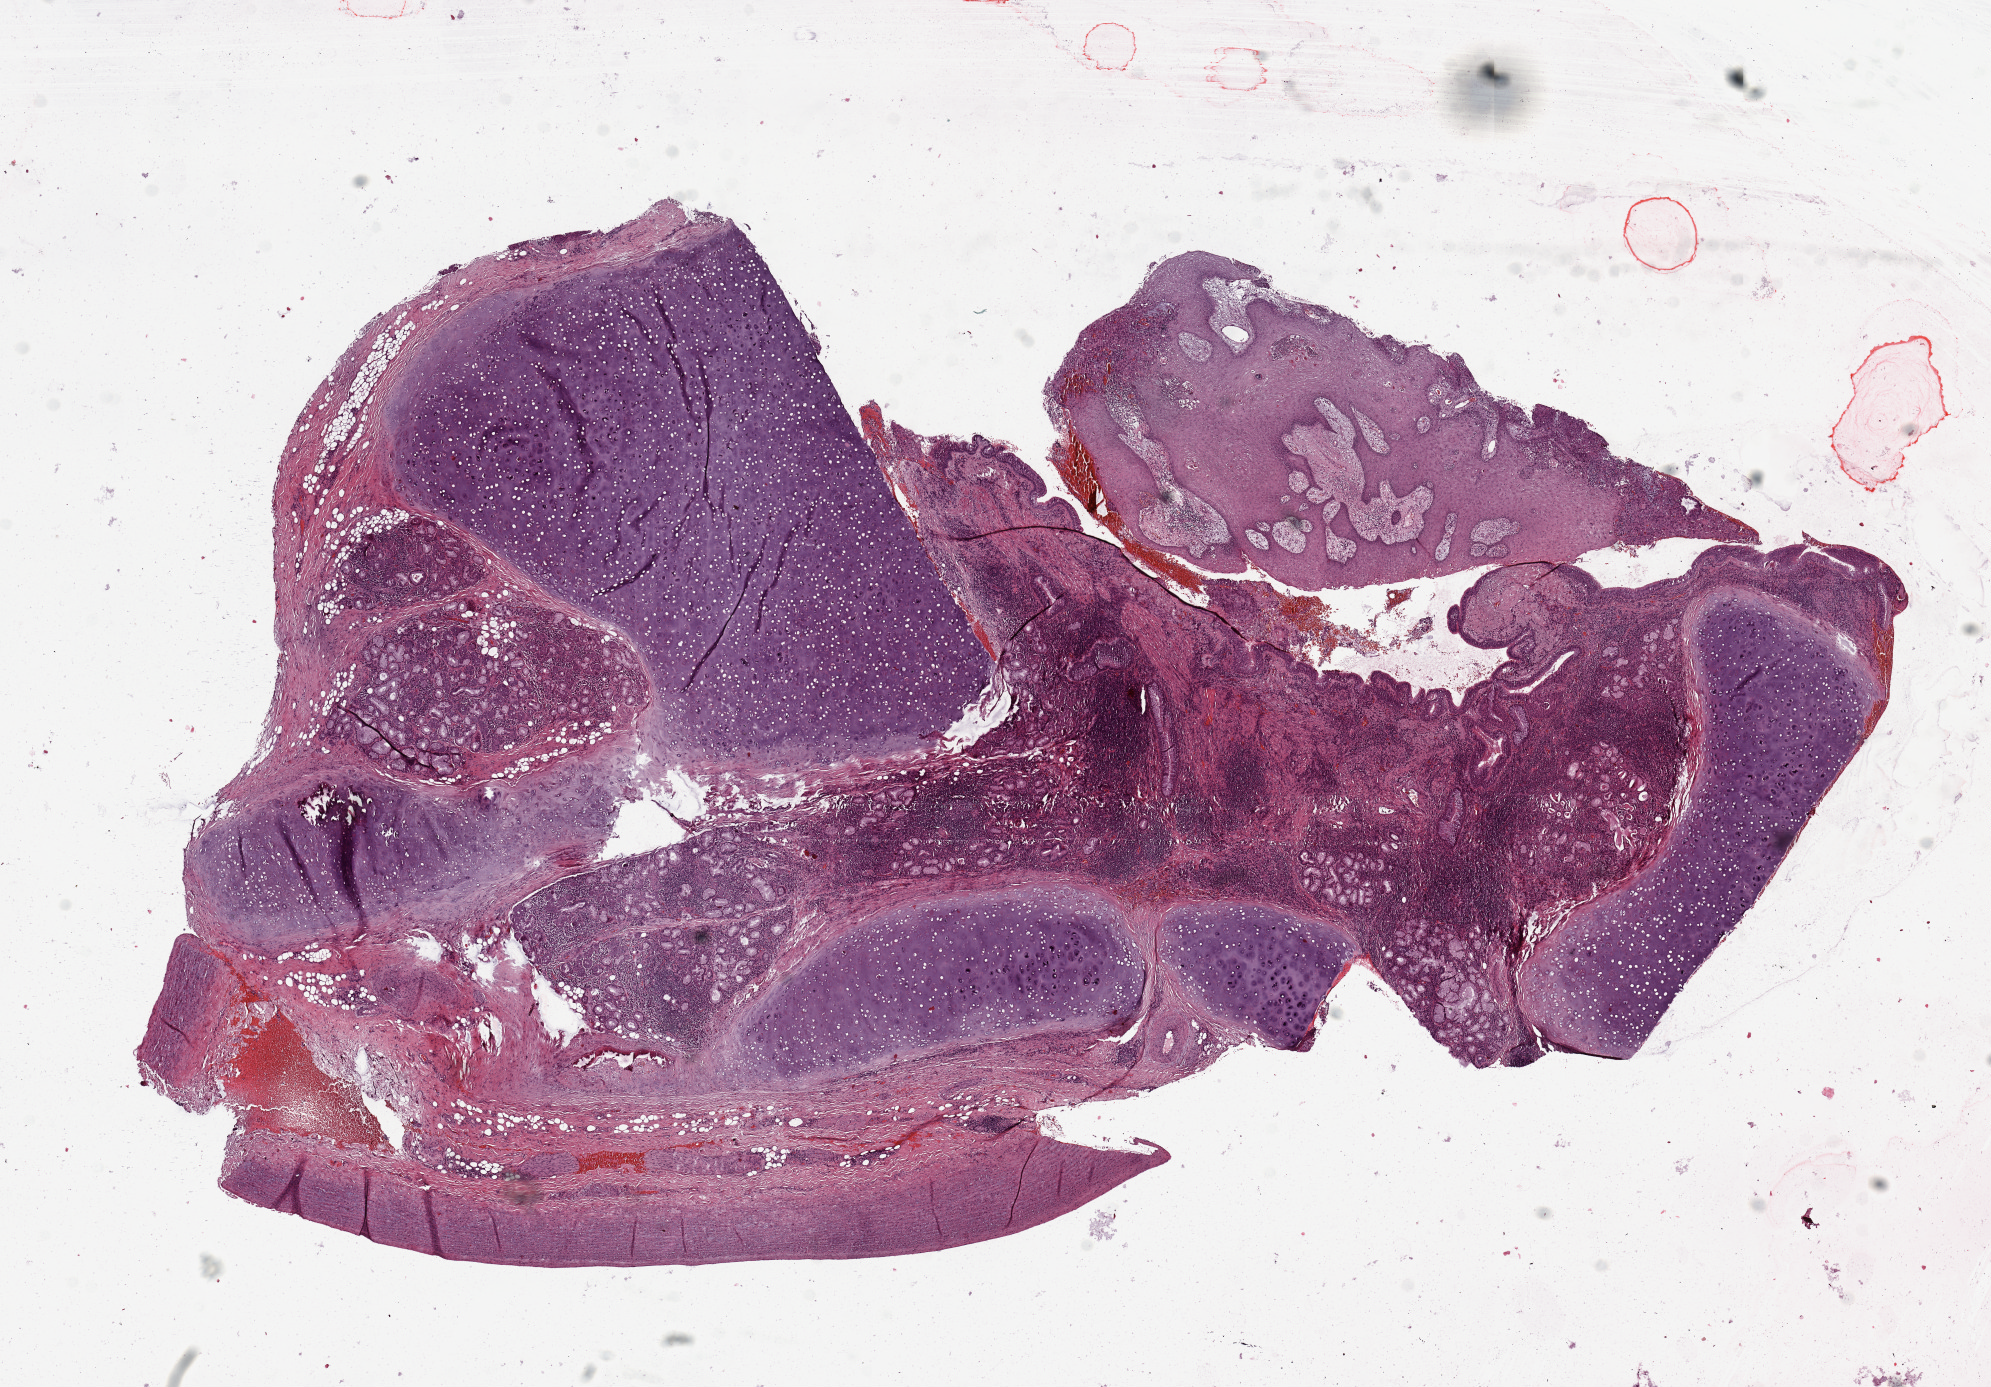
Digitized H&E tissue section (whole slide), whole scanned area (about 15.8 x 11.0 mm, acquisition: 20x scan) shown as a low-resolution overview. Tumour tissue sample, lung. Male, 58 y/o.
Histologic diagnosis: Squamous cell carcinoma, NOS.